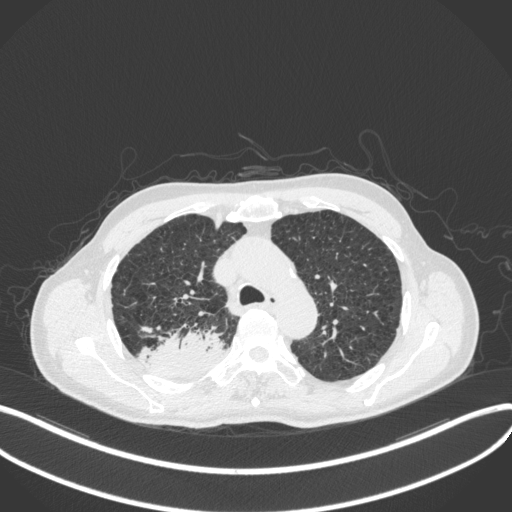
Chest CT, one axial slice. Position 325 of 423 along the scan axis. Reconstruction kernel B31f. 120 kVp. Lung window (W 1500 / L -600 HU). 512 × 512 image matrix, field of view 400 × 400 mm. Male patient, age 79 years. Case-level facts recorded for this patient, not image findings: clinical TNM (as recorded): T3 N0 M0.
Annotated regions visible in this slice (rectangle marked by the reading radiologist):
- lung tumour (recorded histology: adenocarcinoma): bounding box <135,330,224,379> (left, top, right, bottom; pixels)